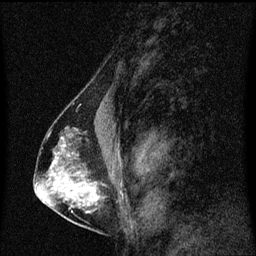
Breast MRI (dynamic contrast-enhanced), one sagittal slice. Position 36 of 60 along the scan axis. Dynamic contrast-enhanced series, image 2 of 3 at this slice position (ordered by acquisition). 1.5 T. TE 4.2 ms, TR 8.4 ms. 2 mm slice thickness. 256 × 256 image matrix, field of view 200 × 200 mm. Patient: female, 40 years. Case-level facts recorded for this patient, not image findings: setting: breast cancer imaged before/during neoadjuvant chemotherapy; receptor status: triple-negative.
Structures marked on this image (semi-automatically segmented with operator editing):
- analysis volume of interest (the breast-tissue region the enhancement analysis was run in; not a lesion): box from (x=44, y=128) to (x=119, y=221) px
- tumour enhancement mask (voxels above the 70 % enhancement threshold inside the analysis volume of interest): (x=63, y=146)–(x=99, y=201)